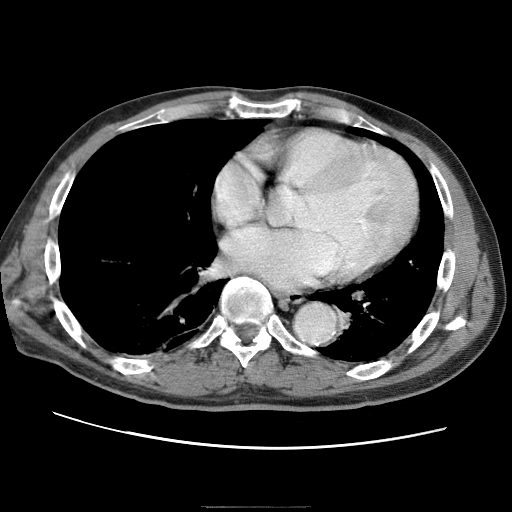
Contrast-enhanced abdominal CT (liver protocol), one axial slice; slice 74 of 75 in the series (ordered by position); one of 2 acquisitions stored at this slice position; soft-tissue window (W 400 / L 40 HU); 512 × 512 image matrix, field of view 360 × 360 mm. From the clinical record (not read from this slice): diagnosis: hepatocellular carcinoma (patient treated with transarterial chemoembolisation; whether this scan precedes or follows treatment is not stated here); TNM stage (as recorded): Stage-II; Child-Pugh class: A; tumour differentiation: well differentiated; tumour size: 2 cm.
Structures marked on this image (semi-automatic segmentation, software-assisted and operator-edited):
- liver parenchyma outside the tumour (the mass and vessels are separate outlines, so this box may not span the whole liver): bounding box (x1, y1, x2, y2) in pixels: (114, 220, 132, 244)